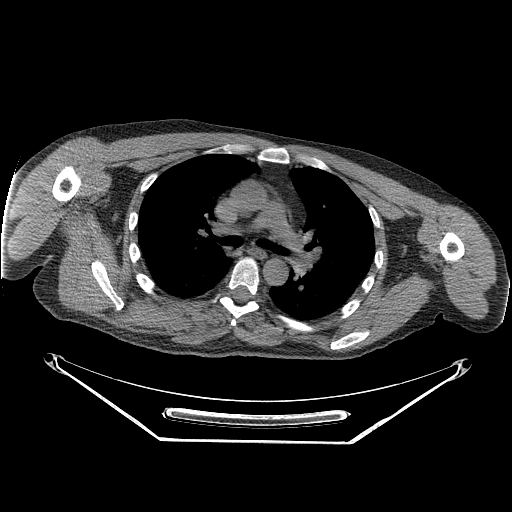
CT of an extremity soft-tissue mass (from a PET/CT study), one axial slice; position 180 of 267 along the scan axis; soft-tissue window (W 400 / L 40 HU); 3.75 mm slice thickness; 512 × 512 image matrix, field of view 500 × 500 mm. Male patient. From the clinical record (not read from this slice): histological type: pleiomorphic spindle cell undifferentiated; grade: high; site of the primary tumour: right parascapusular.
Annotated regions visible in this slice (expert contour drawn on MRI and transferred to this co-registered scan by the dataset authors):
- gross tumour volume including surrounding oedema: bounding box [x1, y1, x2, y2] px = [94, 290, 222, 334]
- gross tumour volume (mass): [121, 292, 161, 325]